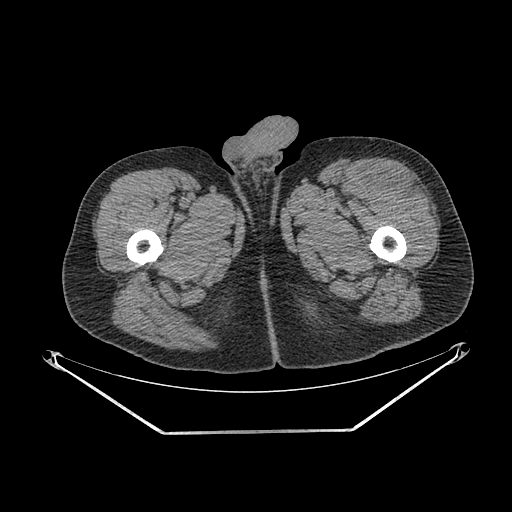
CT of an extremity soft-tissue mass (from a PET/CT study), one axial slice. Slice 258 of 267 in the series (ordered by position). 140 kVp. Soft-tissue window (W 400 / L 40 HU). 512 × 512 image matrix. Male patient. Case-level facts recorded for this patient, not image findings: histological type: extraskeletal osteosarcoma; grade: high; site of the primary tumour: thigh.
Annotated regions visible in this slice (expert contour drawn on MRI and transferred to this co-registered scan by the dataset authors):
- gross tumour volume (mass): bounding box [x1, y1, x2, y2] px = [374, 171, 419, 195]